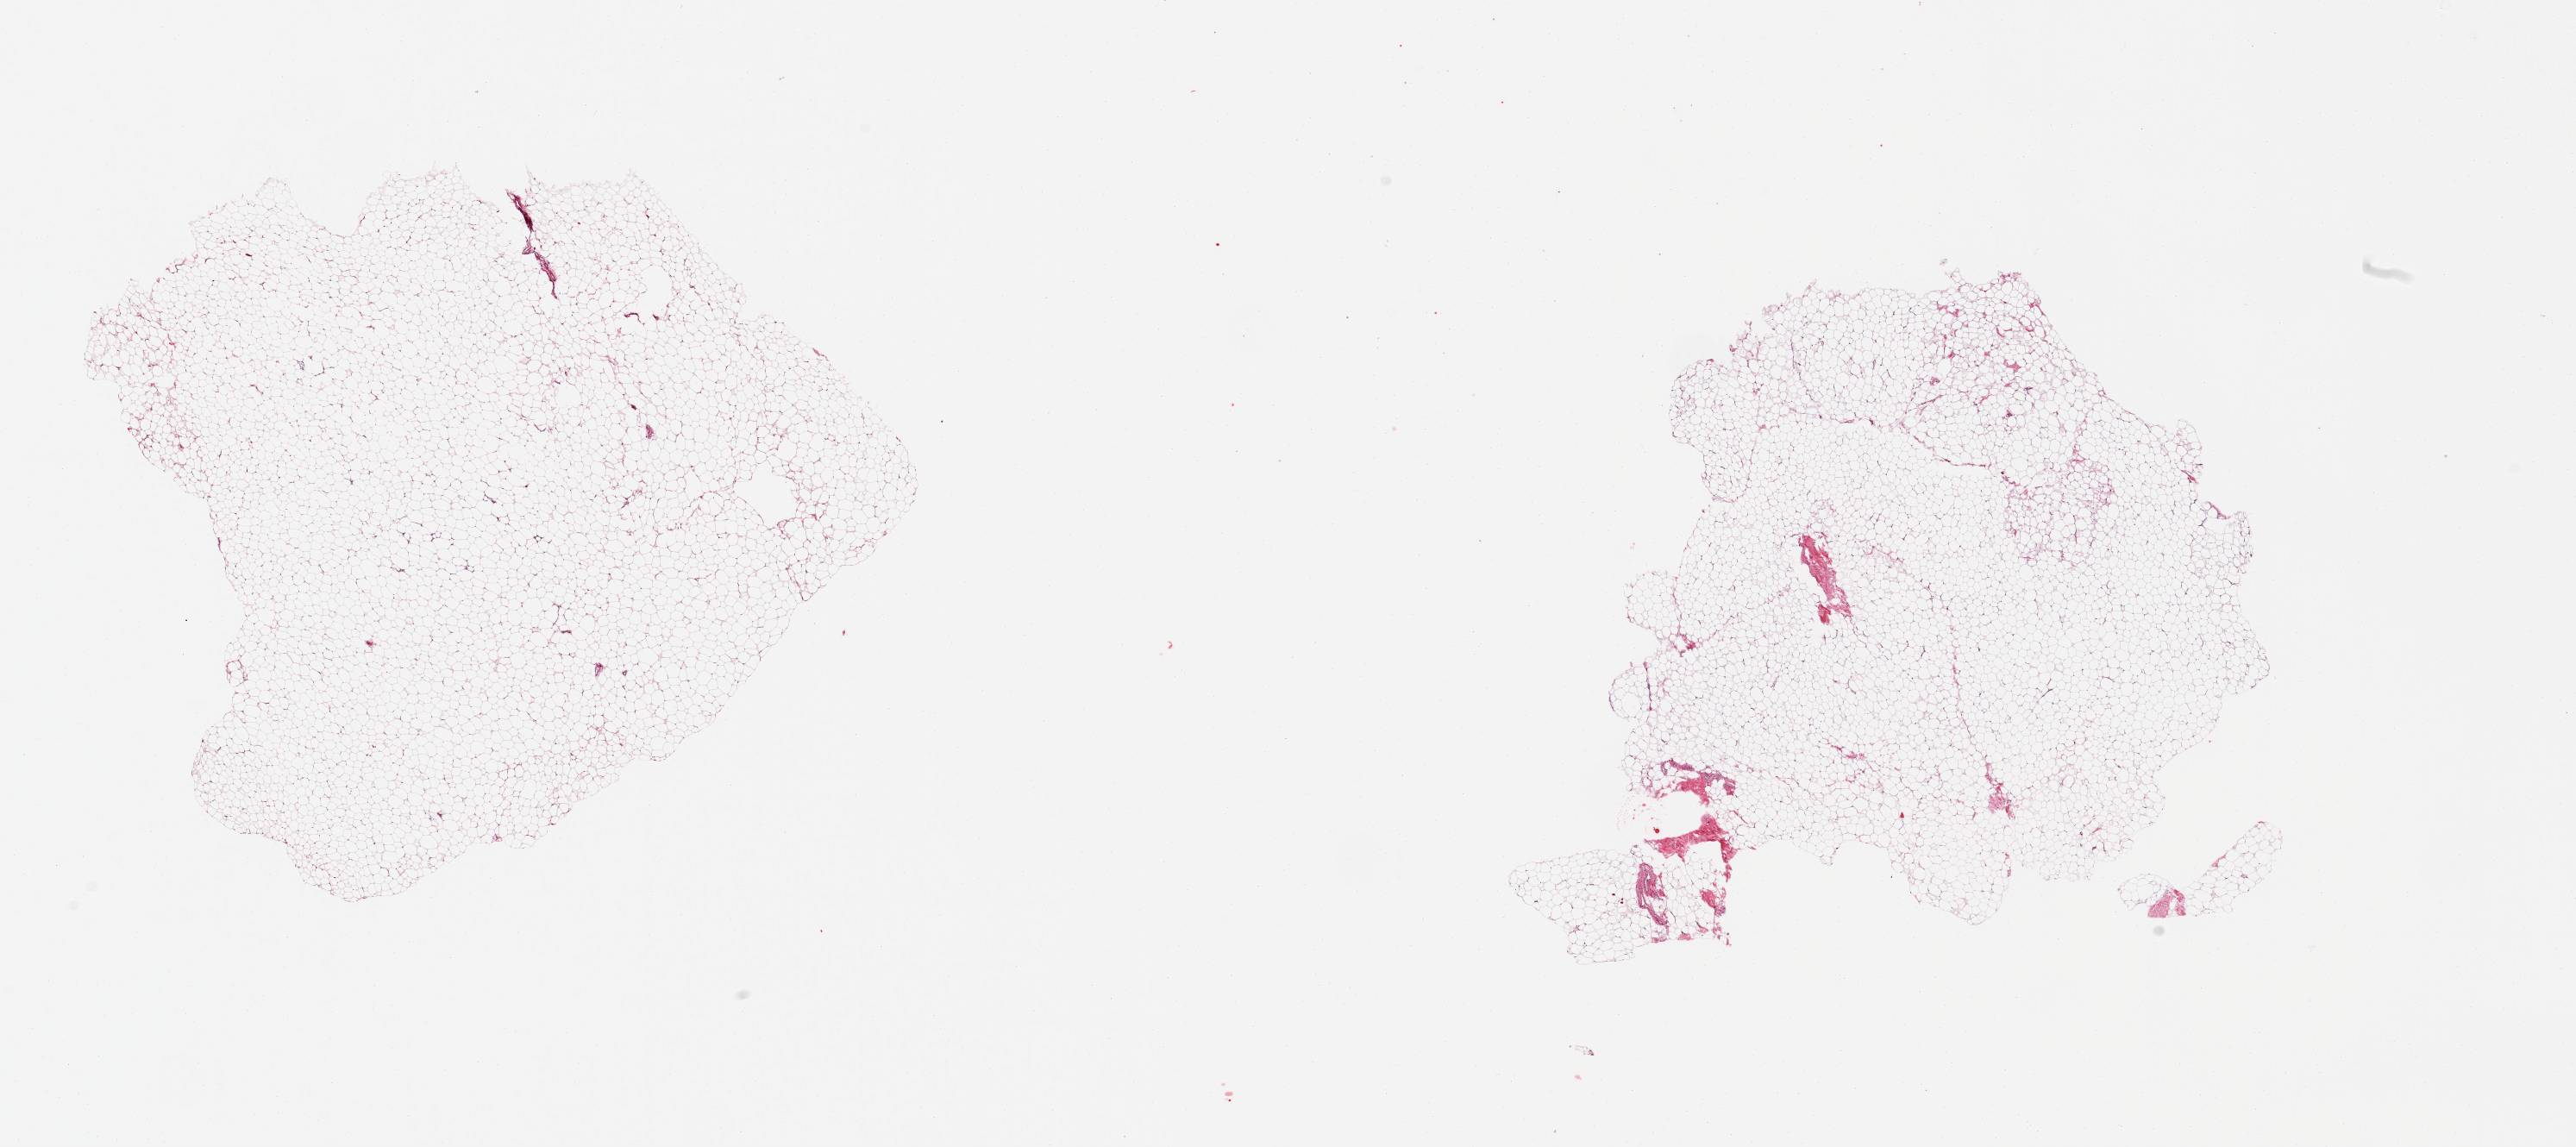
Haematoxylin and eosin whole-slide image, brightfield, shown as a low-resolution overview of the whole scanned area (about 23.6 x 10.5 mm, slide scanned at 20x); PAXgene-fixed paraffin-embedded (PFPE) section; section of breast (target tissue); tissue donor sample.
Pathologist's review note for this sample: 2 pieces; fatty tissue without mammary ducts.